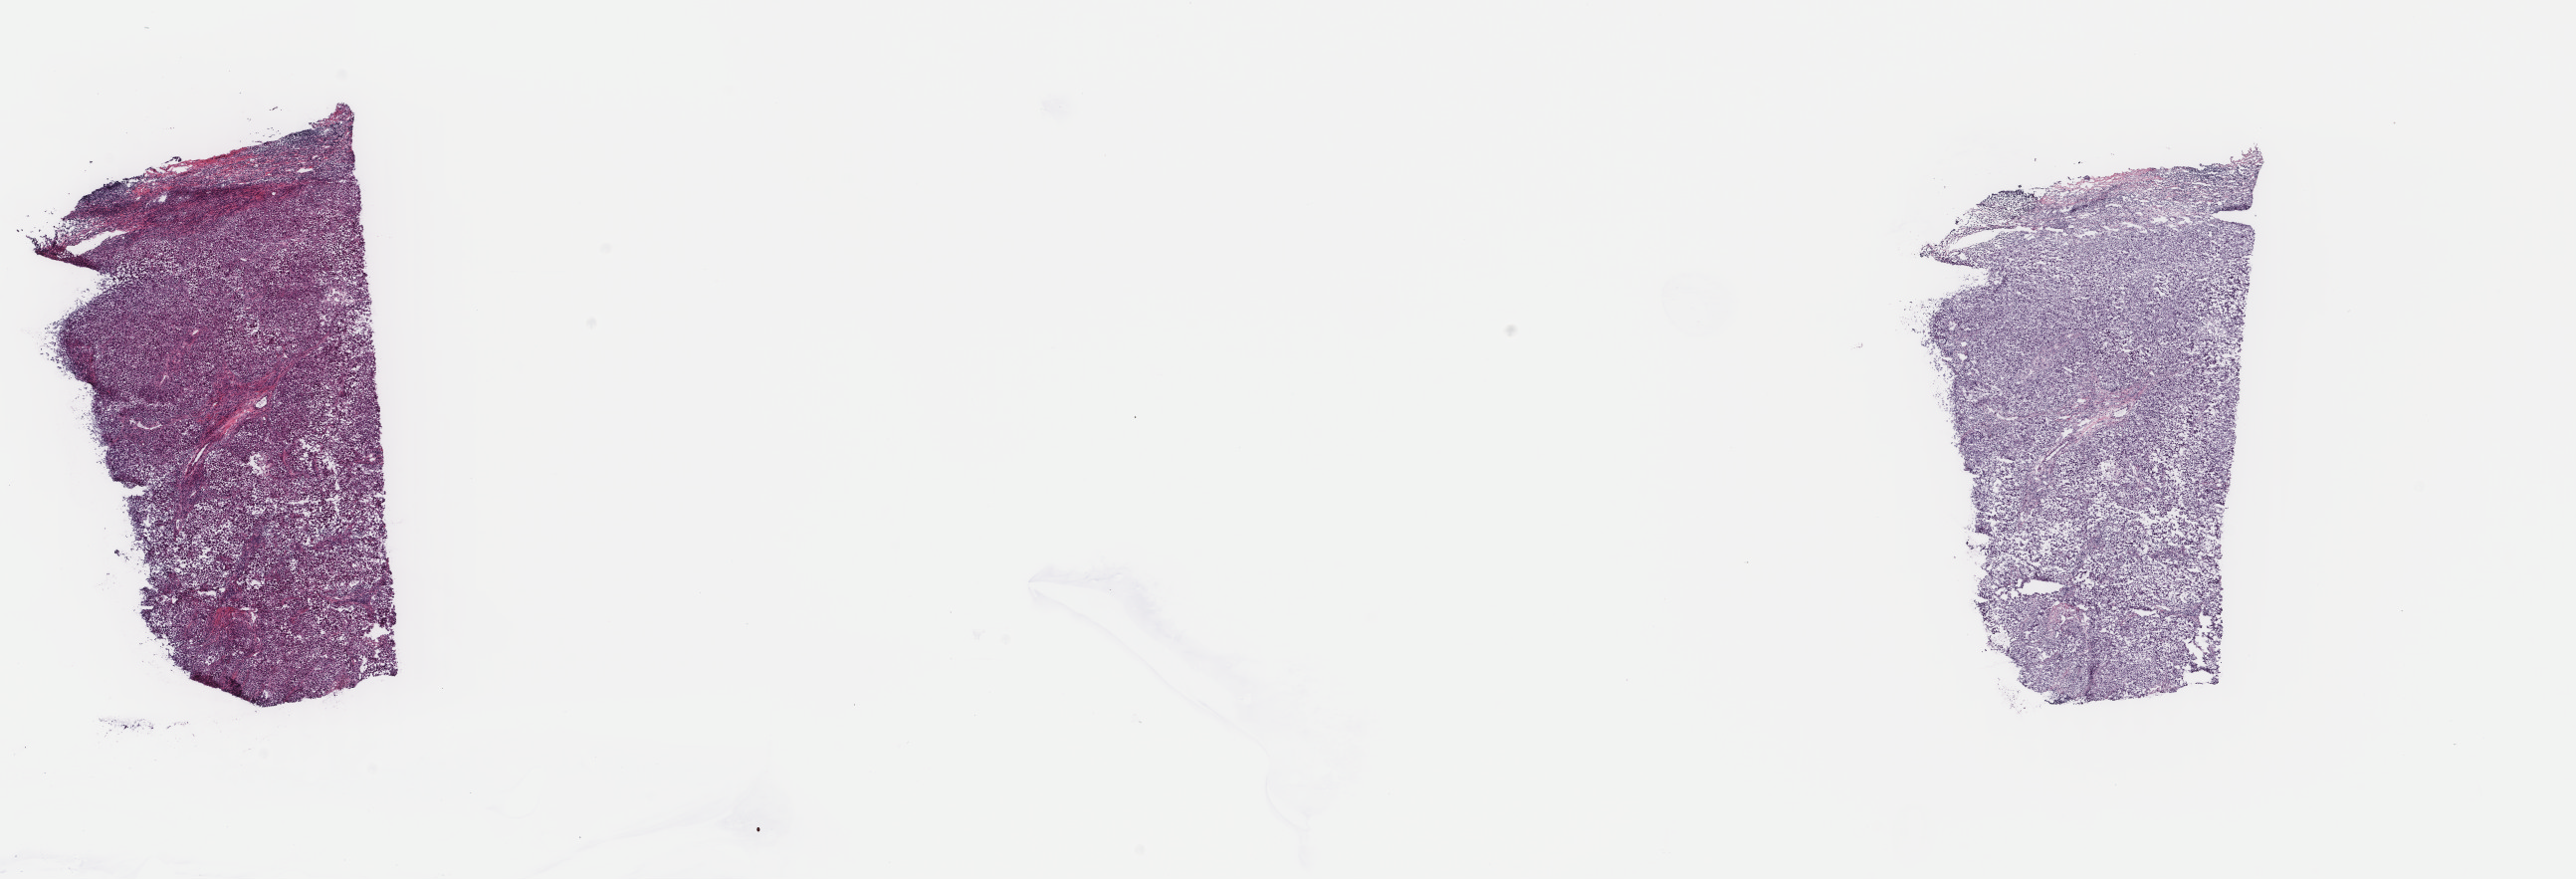
Digitized H&E-stained tissue section (whole slide) — shown as a low-resolution overview of the whole scanned area (about 20.5 x 7.0 mm). Frozen section from the top of the tissue portion. Metastatic tumour sample, sampled site: lymph nodes of head, face and neck. Patient: male, age at initial diagnosis 39 years.
This section: metastatic tumour tissue. Patient diagnosis: Malignant melanoma, NOS.